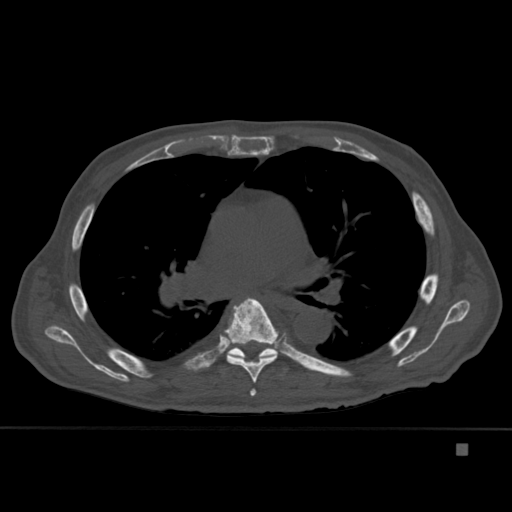
CT including the spine, one axial slice; bone window (W 1800 / L 400 HU); 1.5 mm slice thickness; 512 × 512 image matrix, field of view 378 × 378 mm. Patient: male, 75 years. From the clinical record (not read from this slice): primary cancer: prostate.
Structures marked on this image (semi-automatic segmentation, software-assisted and operator-edited):
- T5 vertebra: bounding box (x1, y1, x2, y2) in pixels: (250, 388, 257, 397)
- T6 vertebra: (224, 297, 279, 383)
- T7 vertebra: (227, 347, 287, 370)